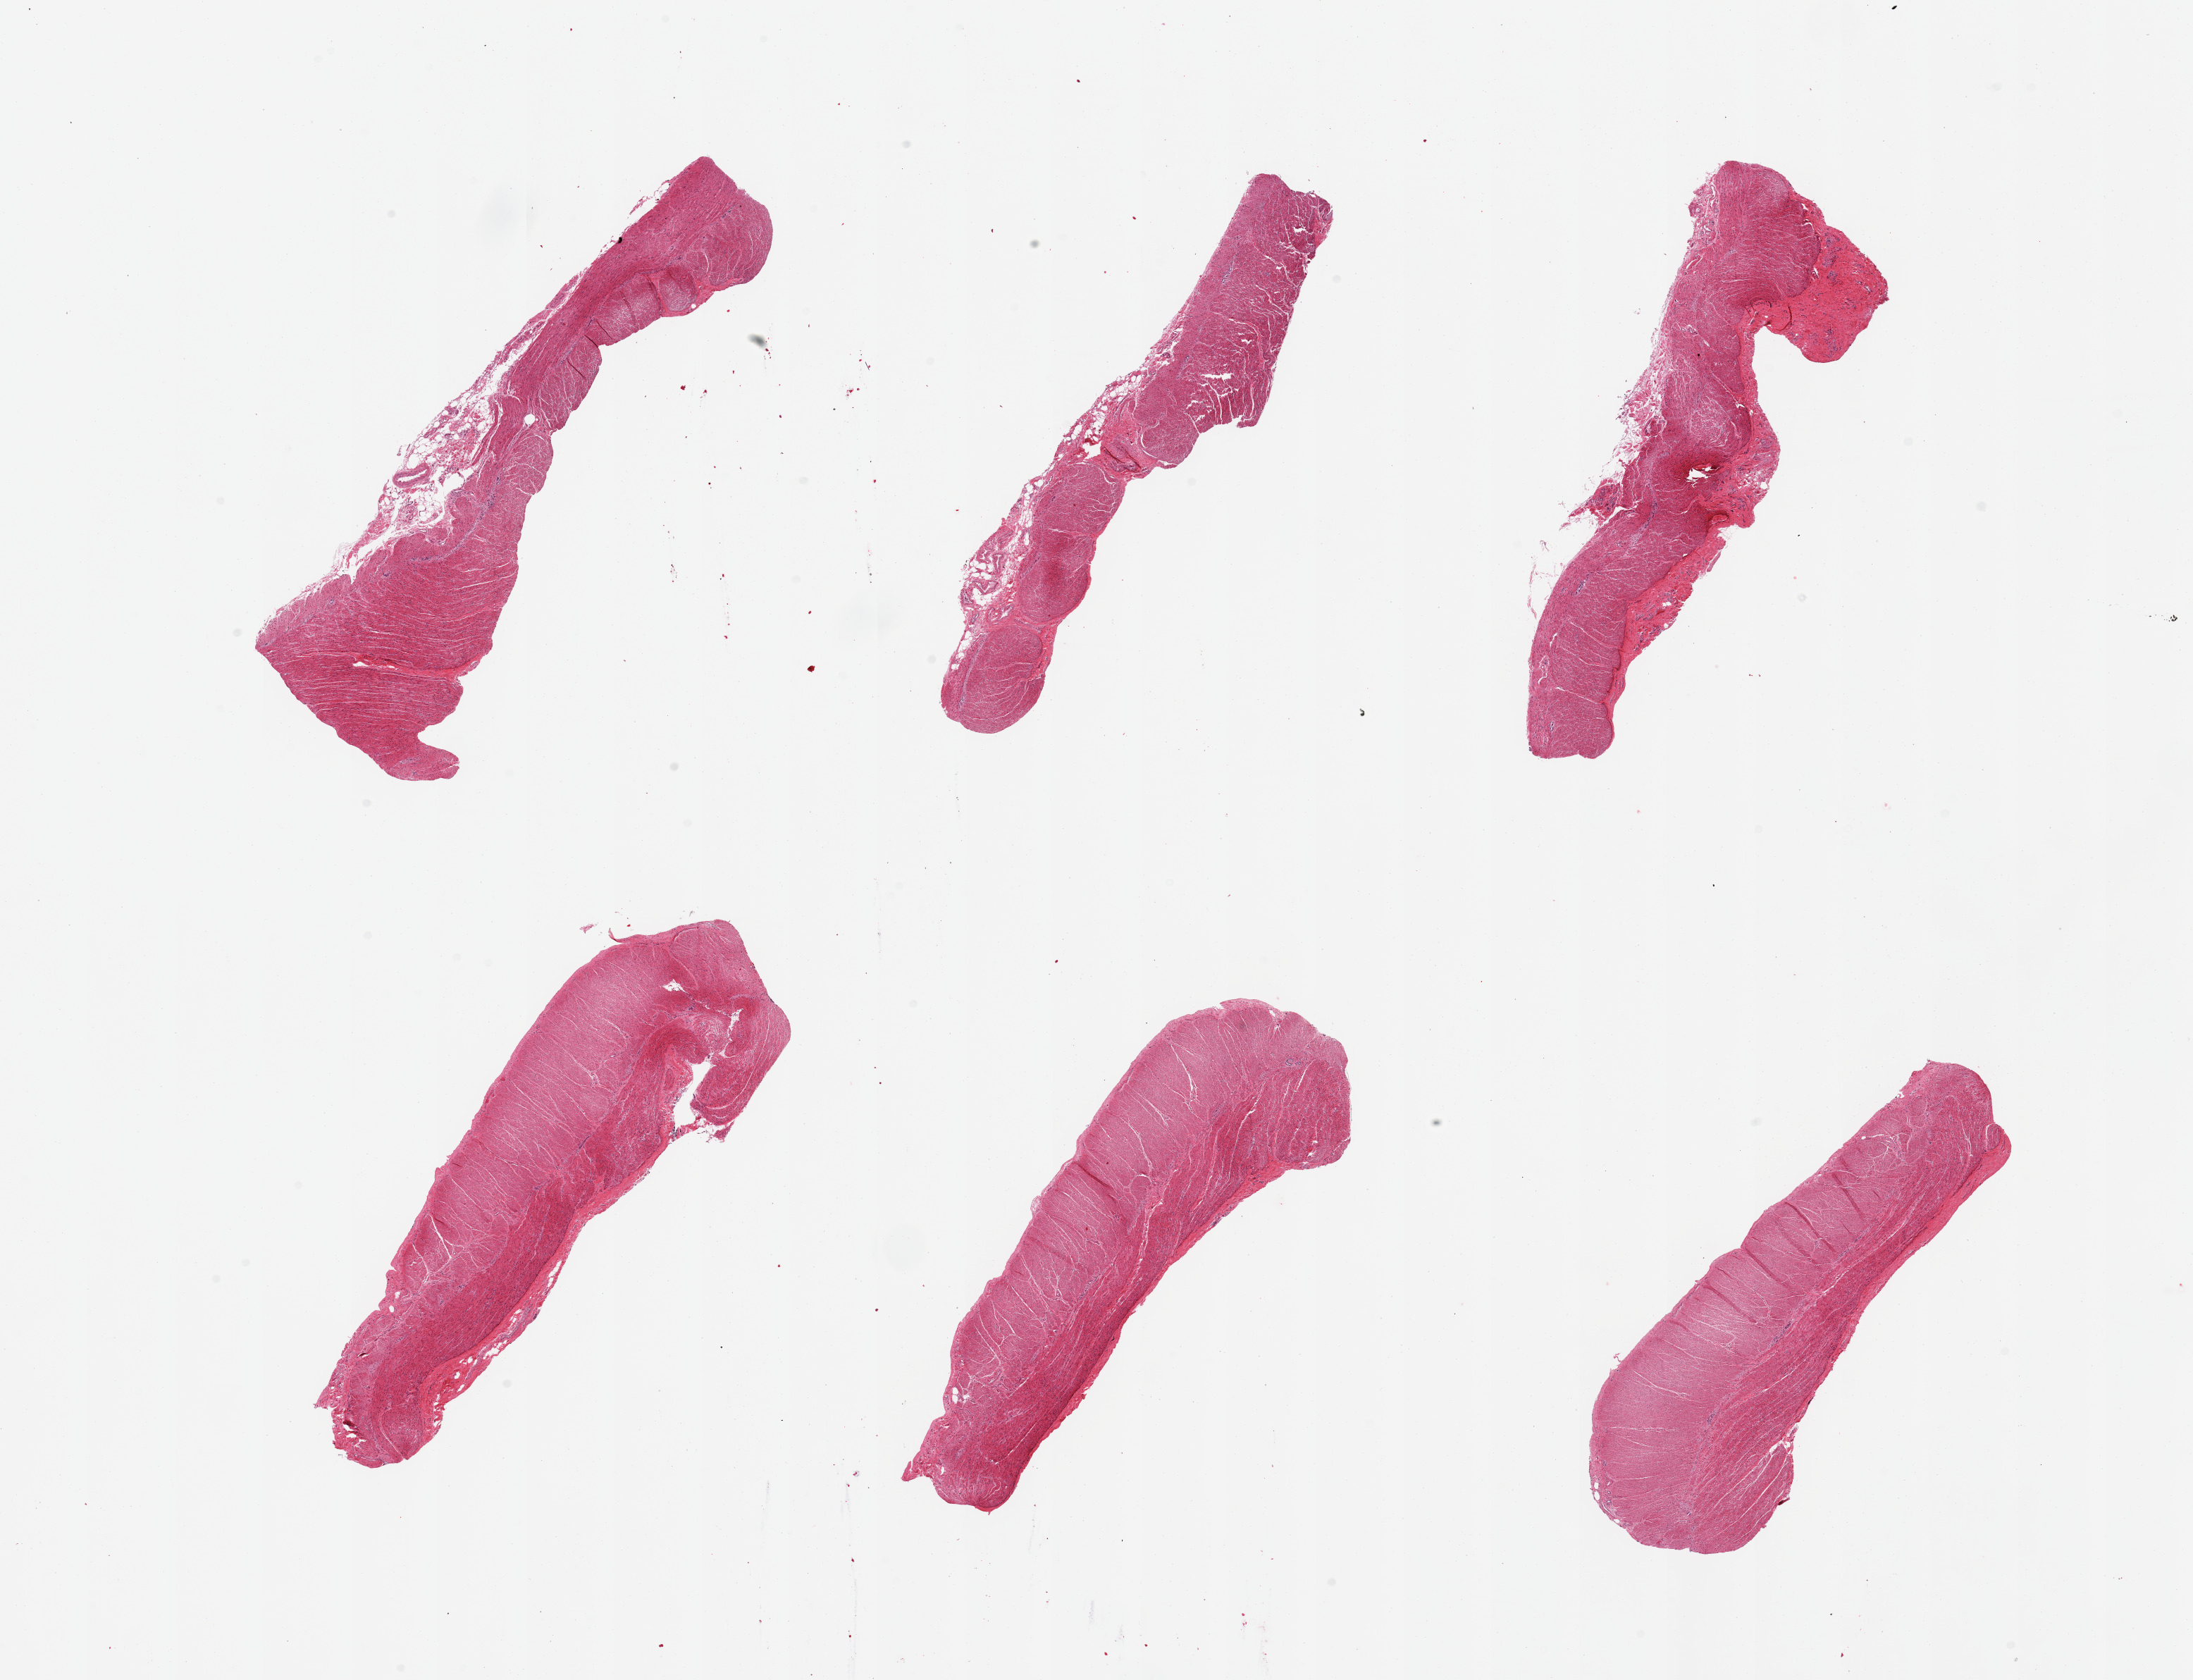
Digitized haematoxylin and eosin-stained section — low-resolution overview of the scanned area, about 24.6 x 18.9 mm (acquisition: 20x scan), PAXgene-fixed, paraffin-embedded tissue, section of sigmoid colon (target tissue), donor tissue sample. Female donor.
Review note (as recorded): 6 pieces.